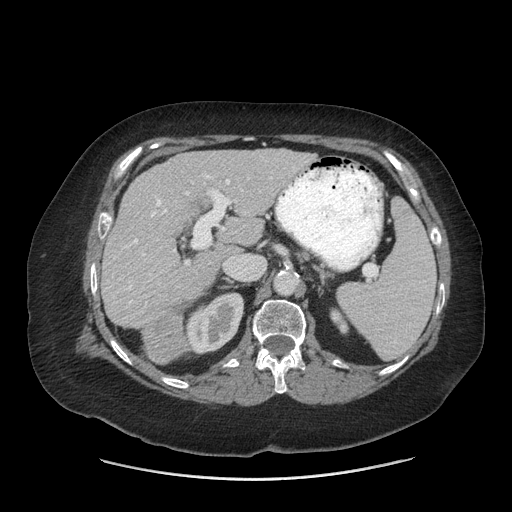
Contrast-enhanced abdominal CT (liver protocol), one axial slice. Position 38 of 69 along the scan axis. Reconstruction kernel STANDARD. 140 kVp. Soft-tissue window (W 400 / L 40 HU). 2.5 mm slice thickness. 512 × 512 image matrix, field of view 420 × 420 mm. Case-level facts recorded for this patient, not image findings: diagnosis: hepatocellular carcinoma (patient treated with transarterial chemoembolisation; whether this scan precedes or follows treatment is not stated here); TNM stage (as recorded): Stage-IIIB.
Outlined on this slice (semi-automatic segmentation, software-assisted and operator-edited):
- liver parenchyma outside the tumour (the mass and vessels are separate outlines, so this box may not span the whole liver): bounding box [x1, y1, x2, y2] px = [102, 148, 315, 328]
- mass: [144, 308, 184, 364]
- liver vessels: [125, 175, 243, 303]